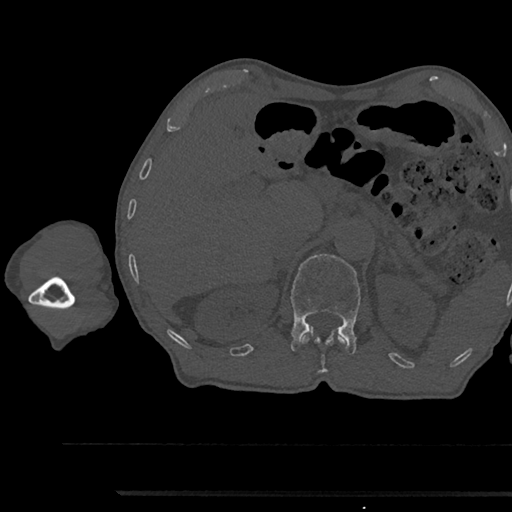
CT including the spine, one axial slice; reconstruction kernel Br40s/3; 120 kVp; bone window (W 1800 / L 400 HU); 0.5 mm slice thickness; 512 × 512 image matrix. Male patient, age 79 years. Case-level facts recorded for this patient, not image findings: primary cancer: prostate.
Structures marked on this image (semi-automatically segmented with operator editing):
- L1 vertebra: bounding box <291,254,361,354> (left, top, right, bottom; pixels)
- T12 vertebra: <301,333,406,372>